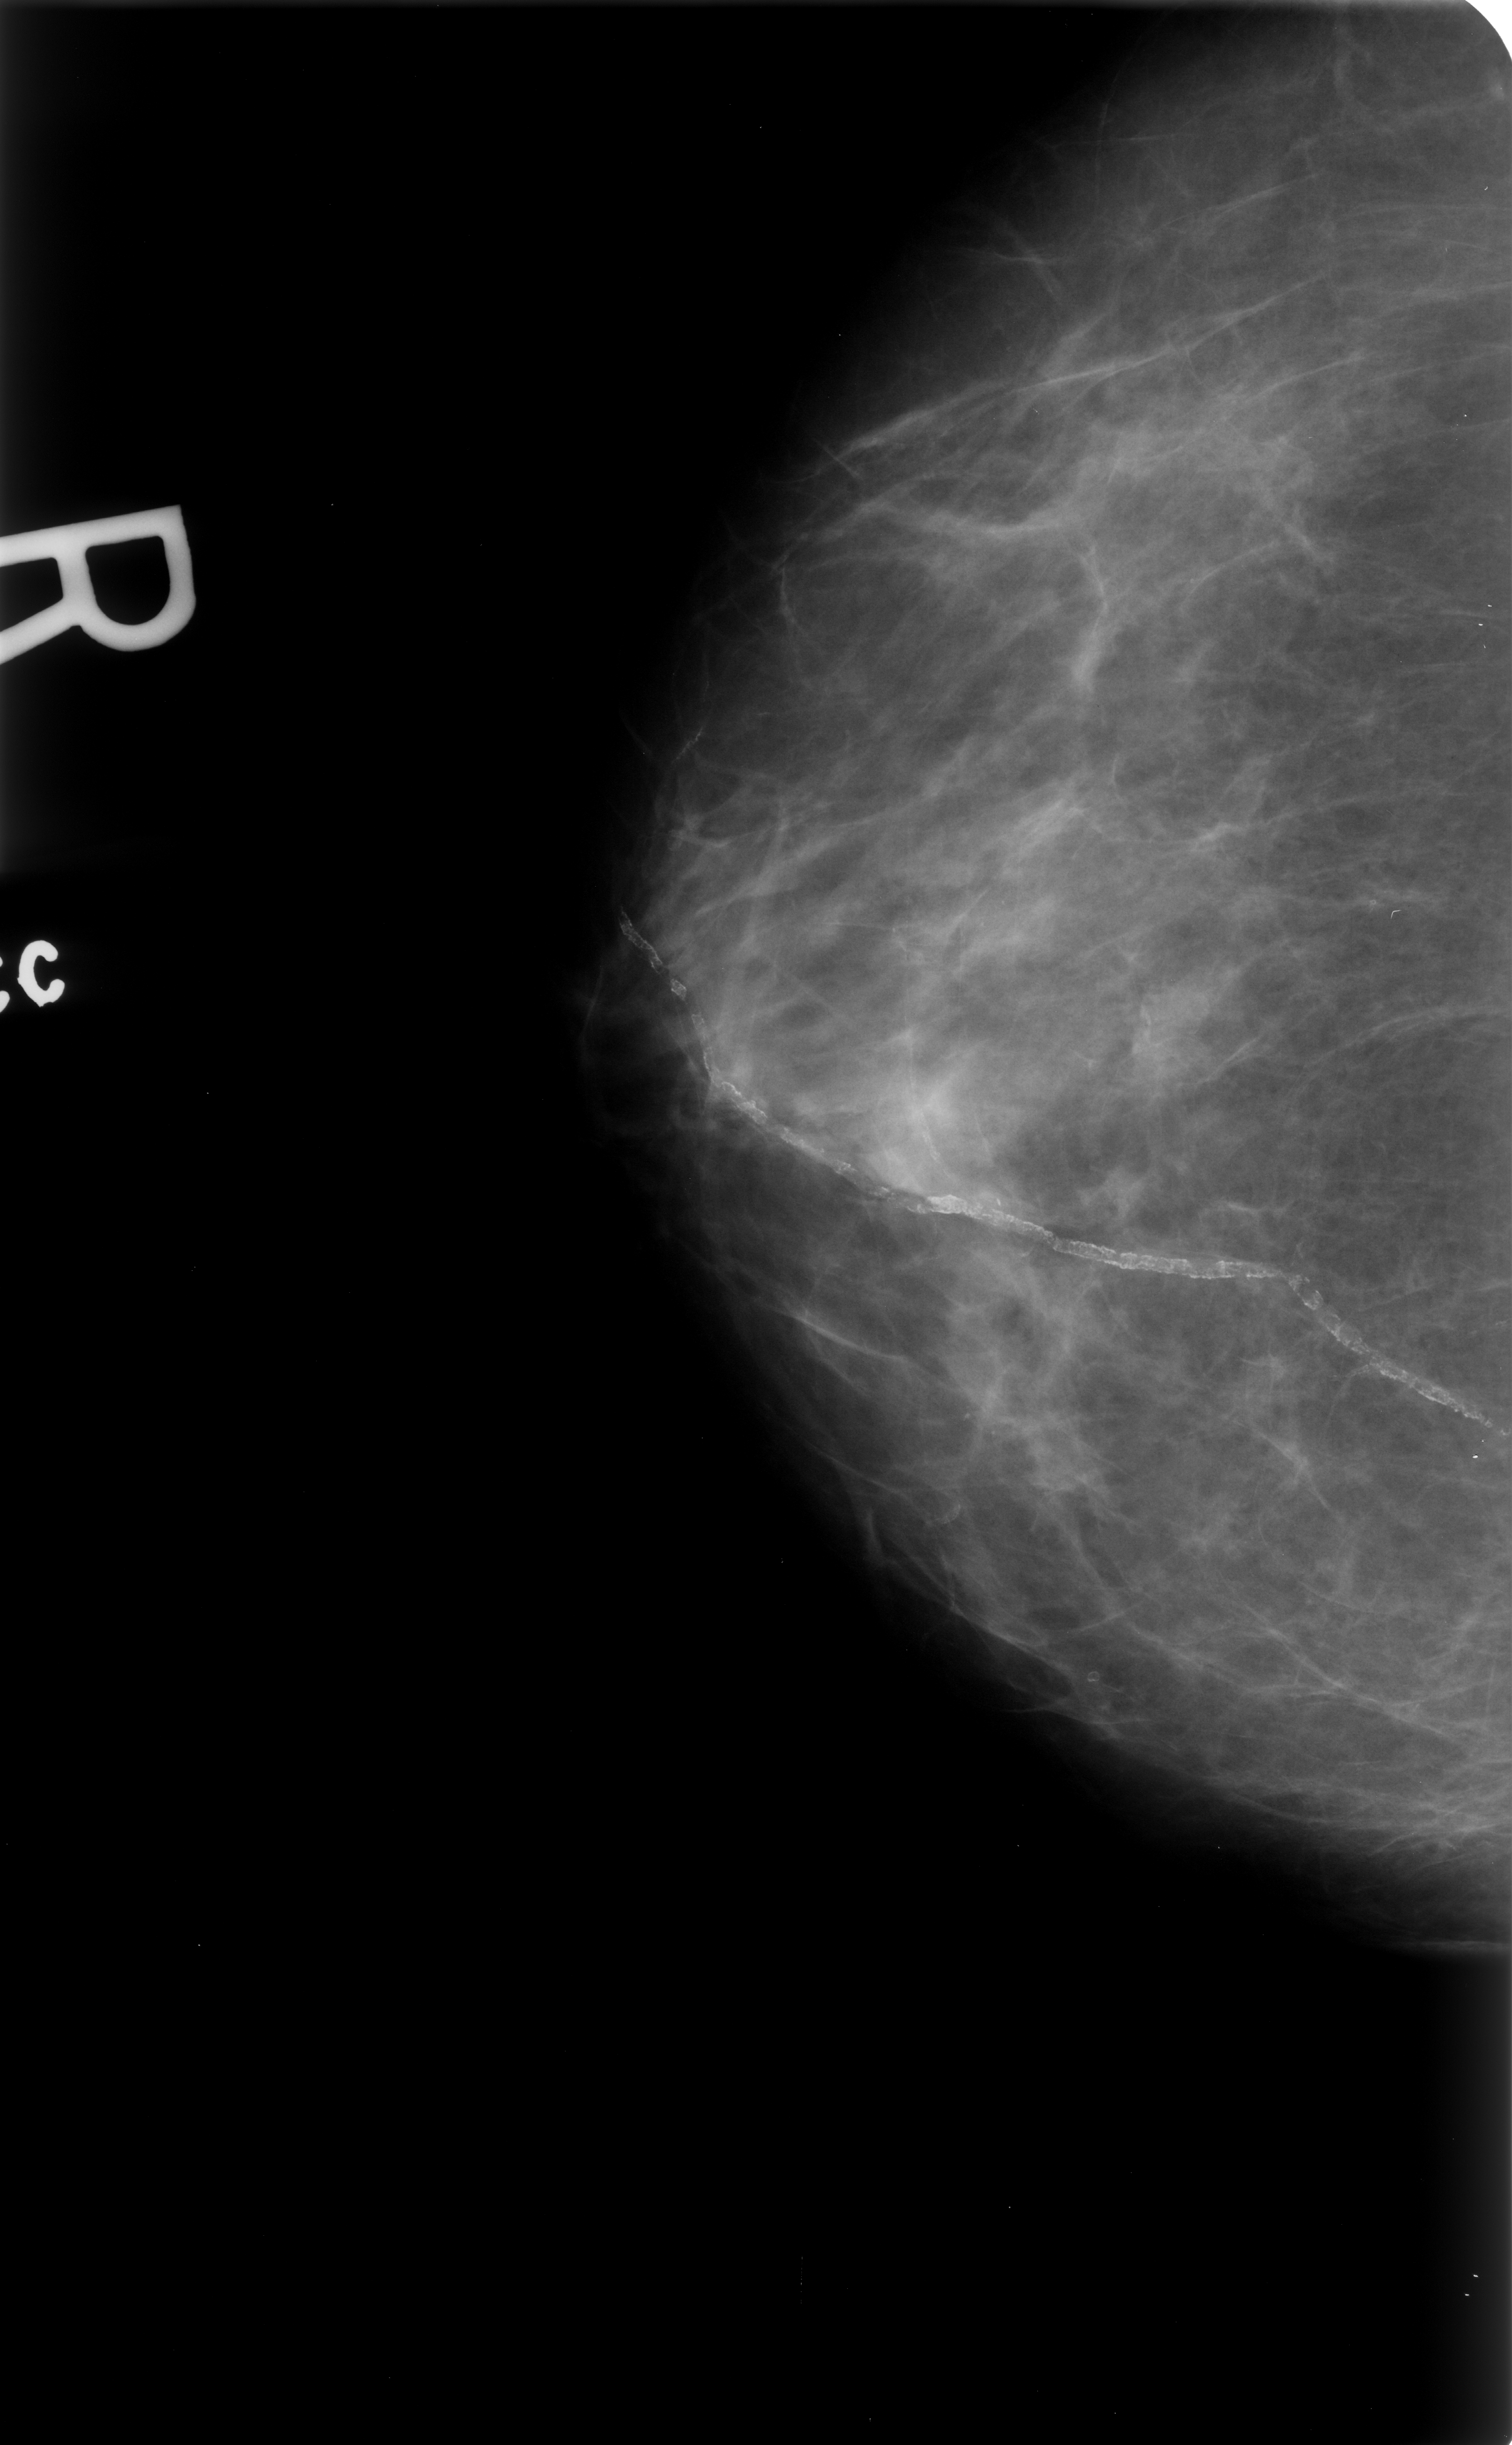
Digitized screen-film mammogram, right breast, CC view, BI-RADS breast density category 2 (scale 1–4).
Abnormality record for this image: calcifications, morphology vascular; BI-RADS assessment category 2; benign without callback (not worked up further).